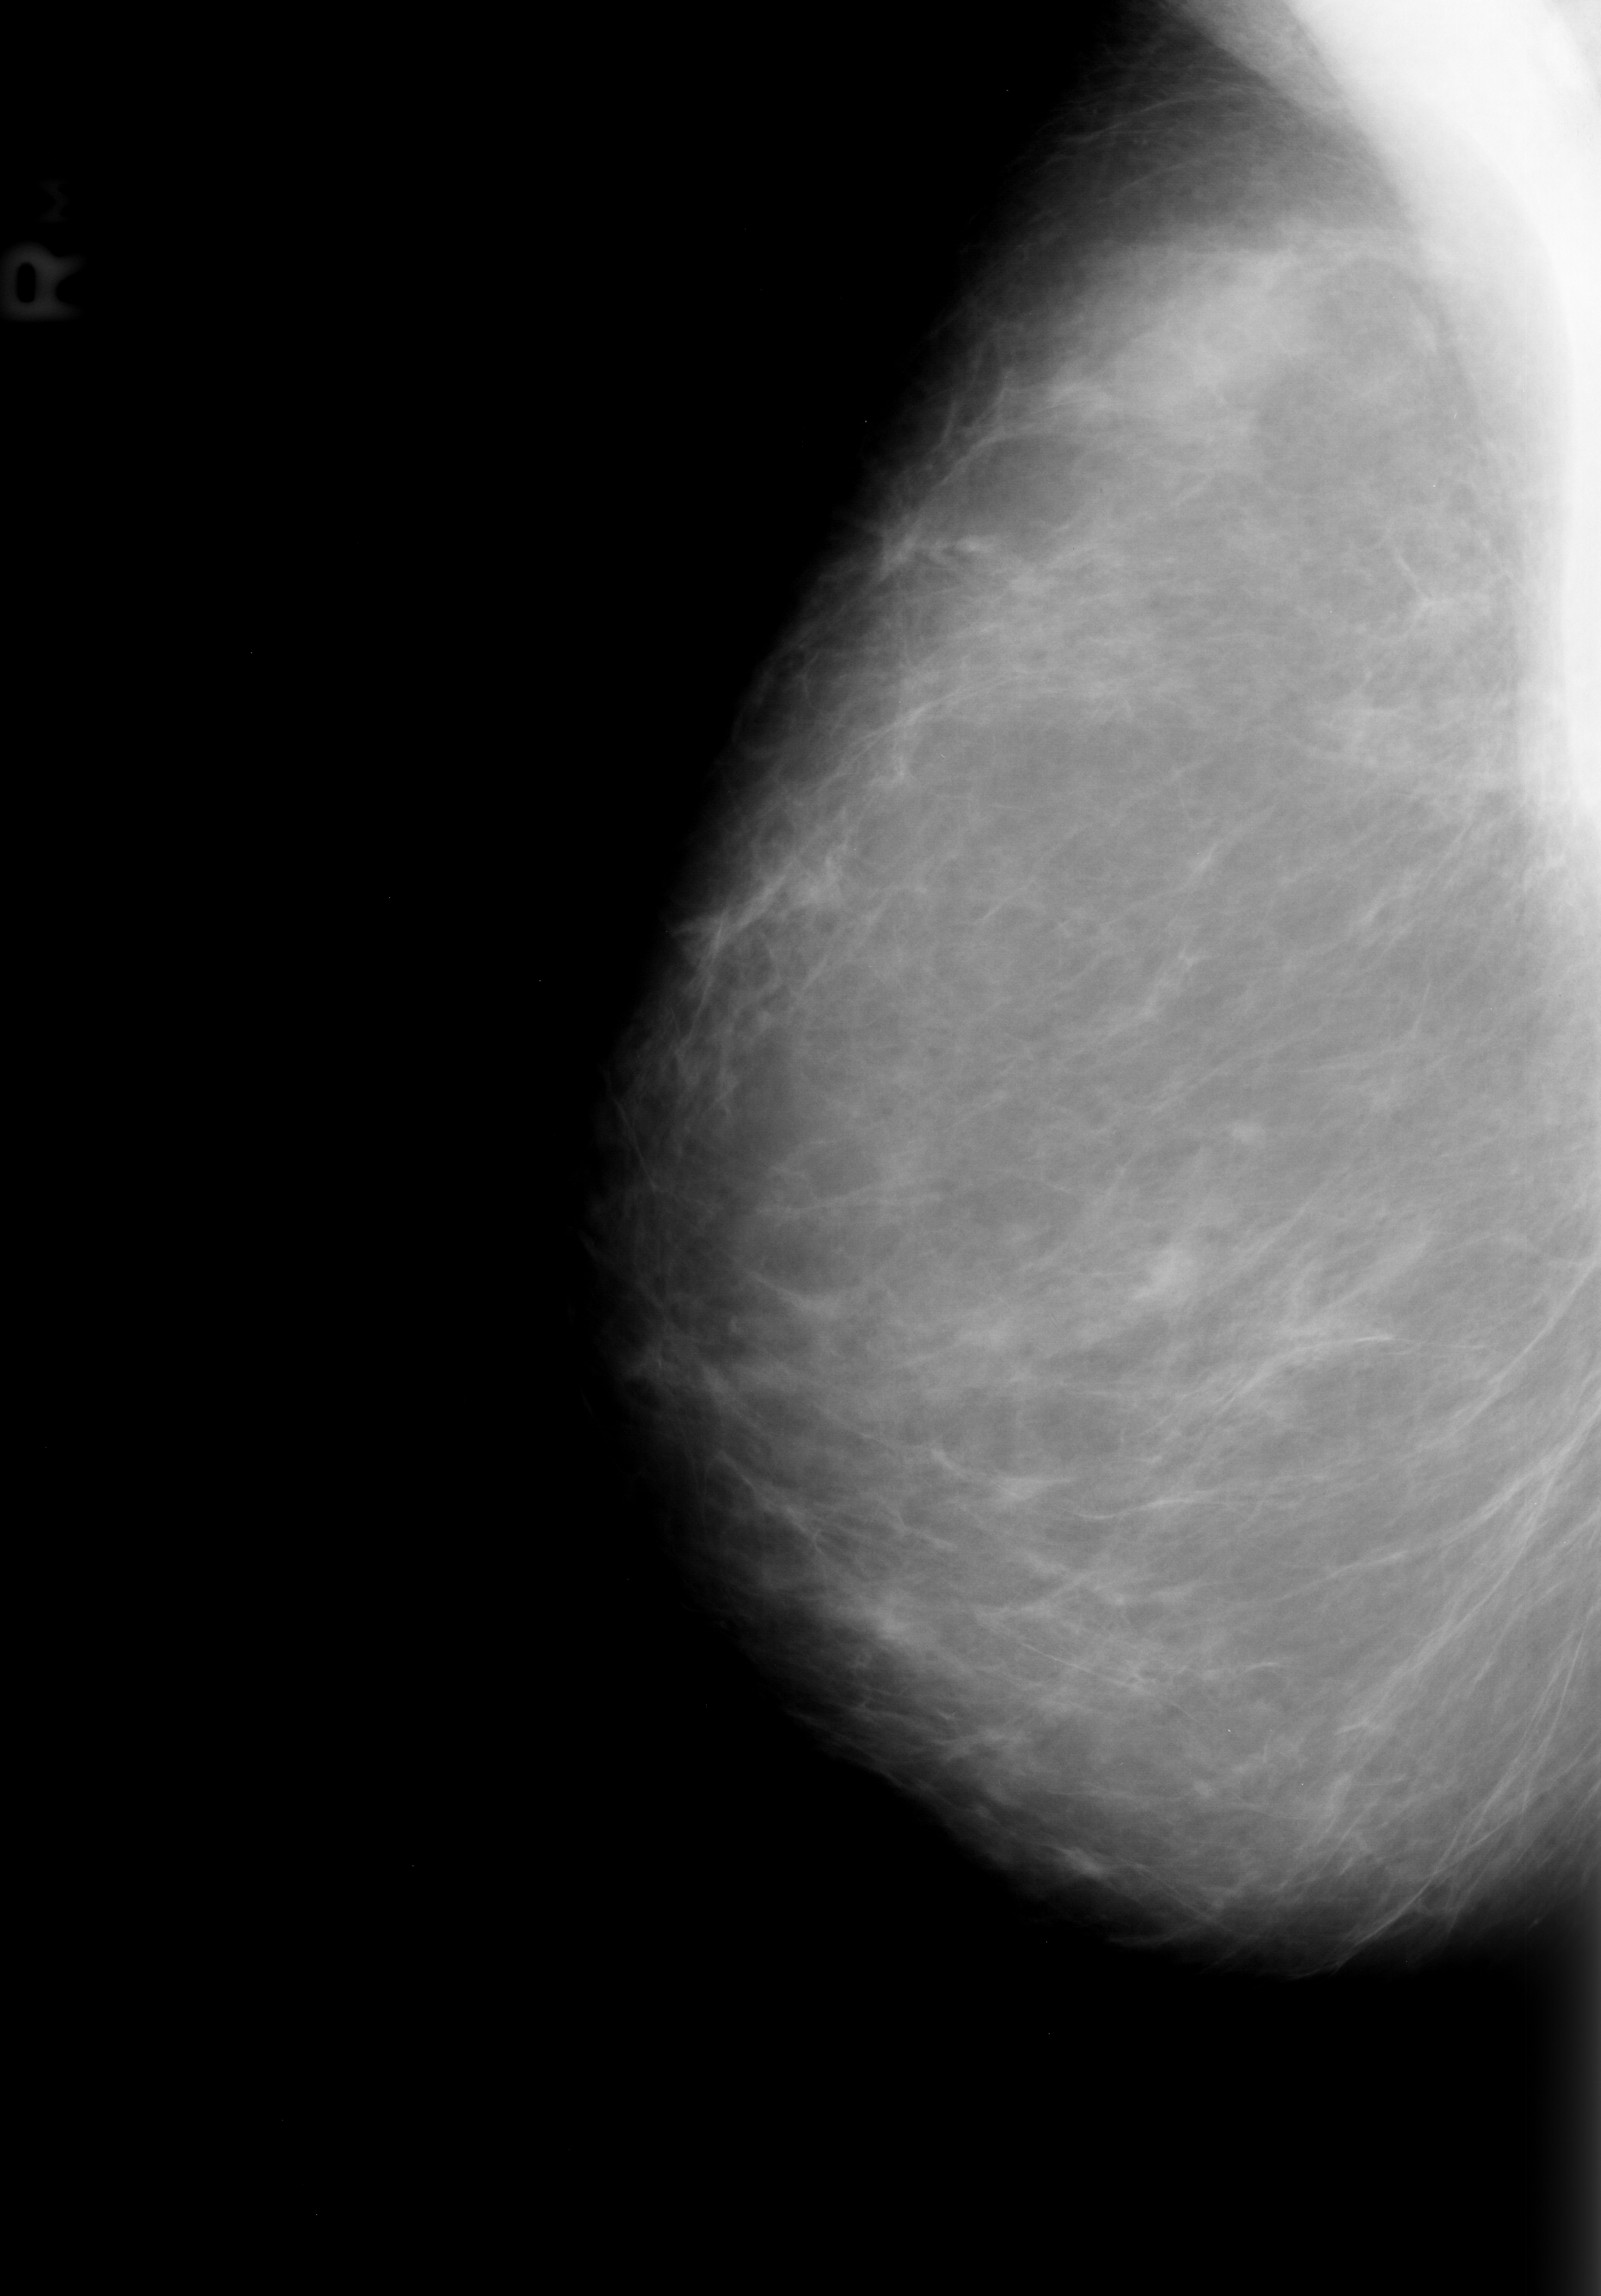
Mammogram (digitized film); right breast; mediolateral oblique (MLO) view; BI-RADS breast density category 2 (scale 1–4).
- Finding: mass, shape asymmetric breast tissue; BI-RADS assessment category 2; benign without callback (not worked up further).